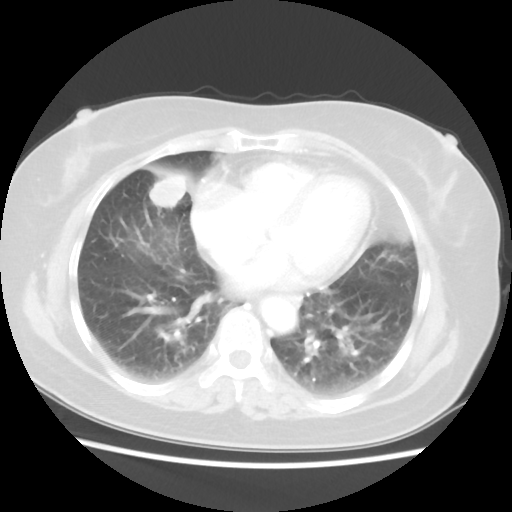
Chest CT, one axial slice; slice 20 of 48 in the series (ordered by position); 100 kVp; lung window (W 1500 / L -600 HU); 512 × 512 image matrix, field of view 343 × 343 mm. Patient: female, 61 years. From the clinical record (not read from this slice): clinical TNM (as recorded): T1c N0 M0.
Structures marked on this image (bounding box drawn by a radiologist):
- lung tumour (recorded histology: adenocarcinoma): bounding box <143,167,188,215> (left, top, right, bottom; pixels)